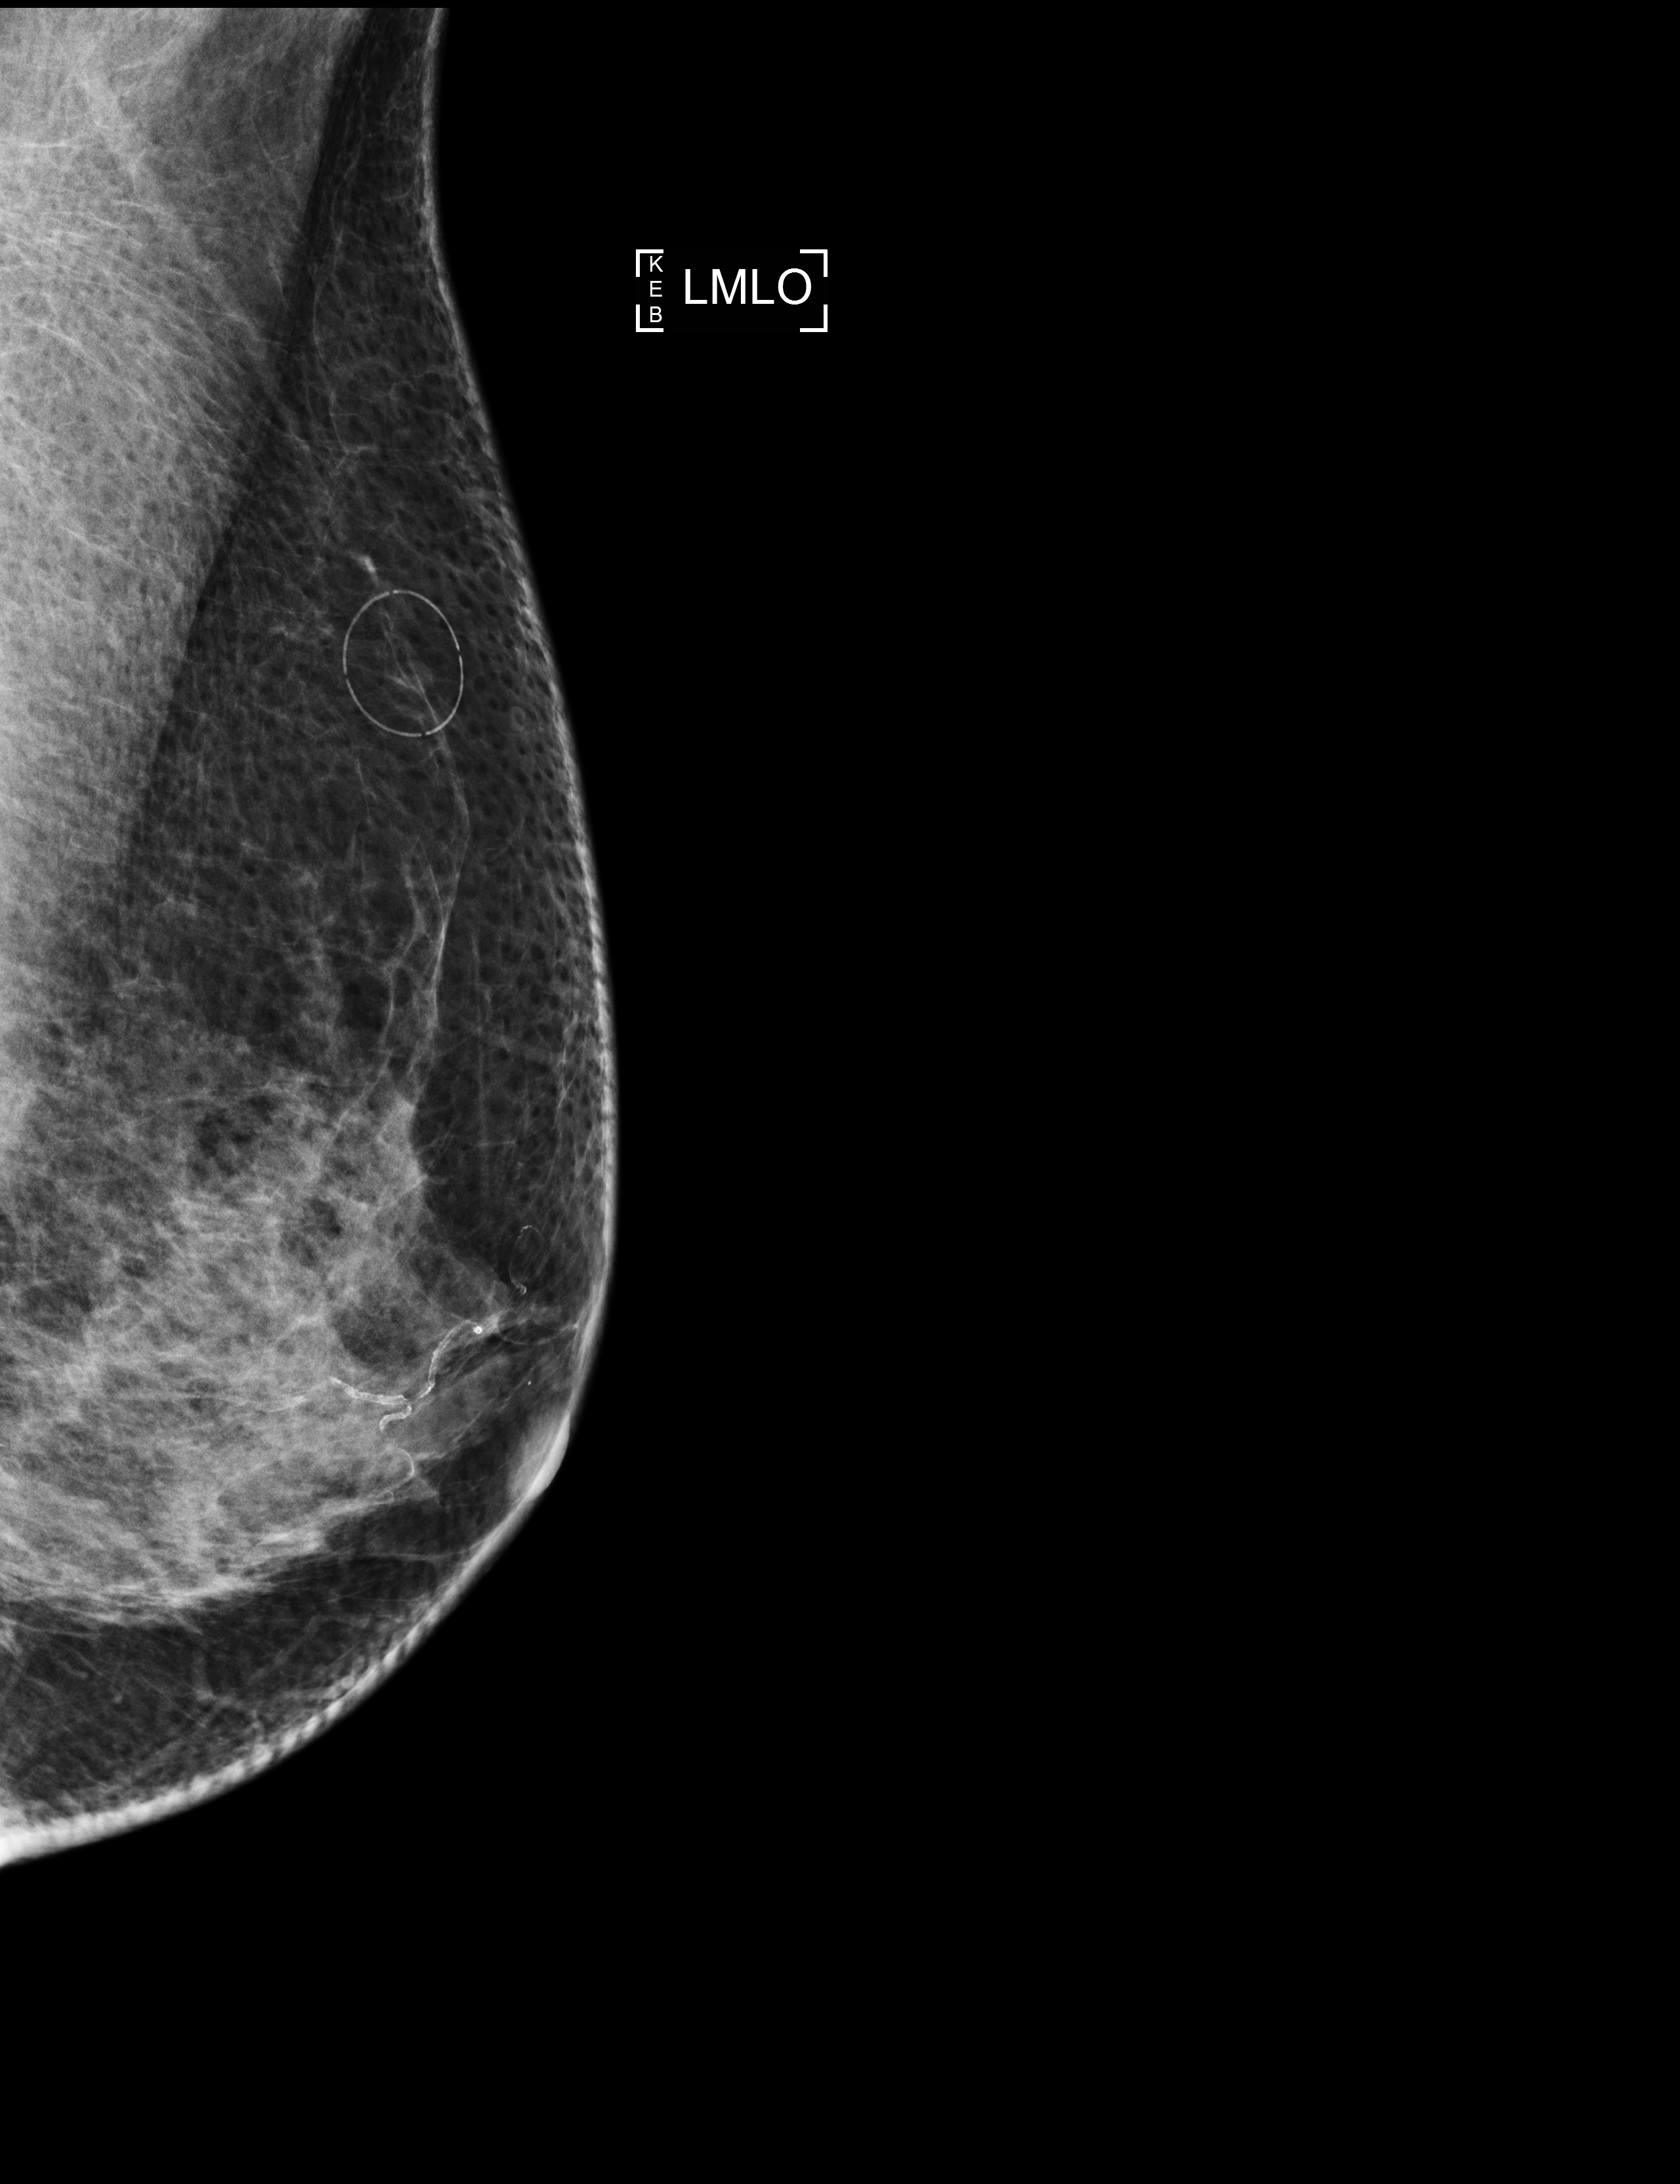
Screening examination. Patient: female, 65 years.
Image type: full-field digital mammogram. Breast: left. Projection: MLO view.